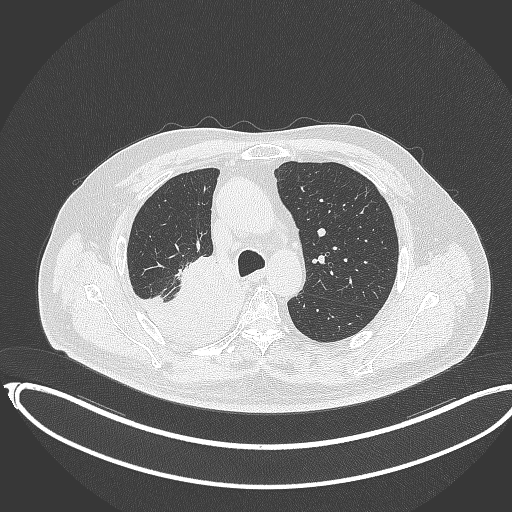
Chest CT, one axial slice. Position 251 of 403 along the scan axis. Reconstruction kernel B70f. Lung window (W 1500 / L -600 HU). 512 × 512 image matrix. Patient: male, 68 years. Case-level facts recorded for this patient, not image findings: clinical TNM (as recorded): T2a N0 M0.
Outlined on this slice (bounding box drawn by a radiologist):
- lung tumour (recorded histology: adenocarcinoma): bounding box [x1, y1, x2, y2] px = [122, 258, 244, 355]